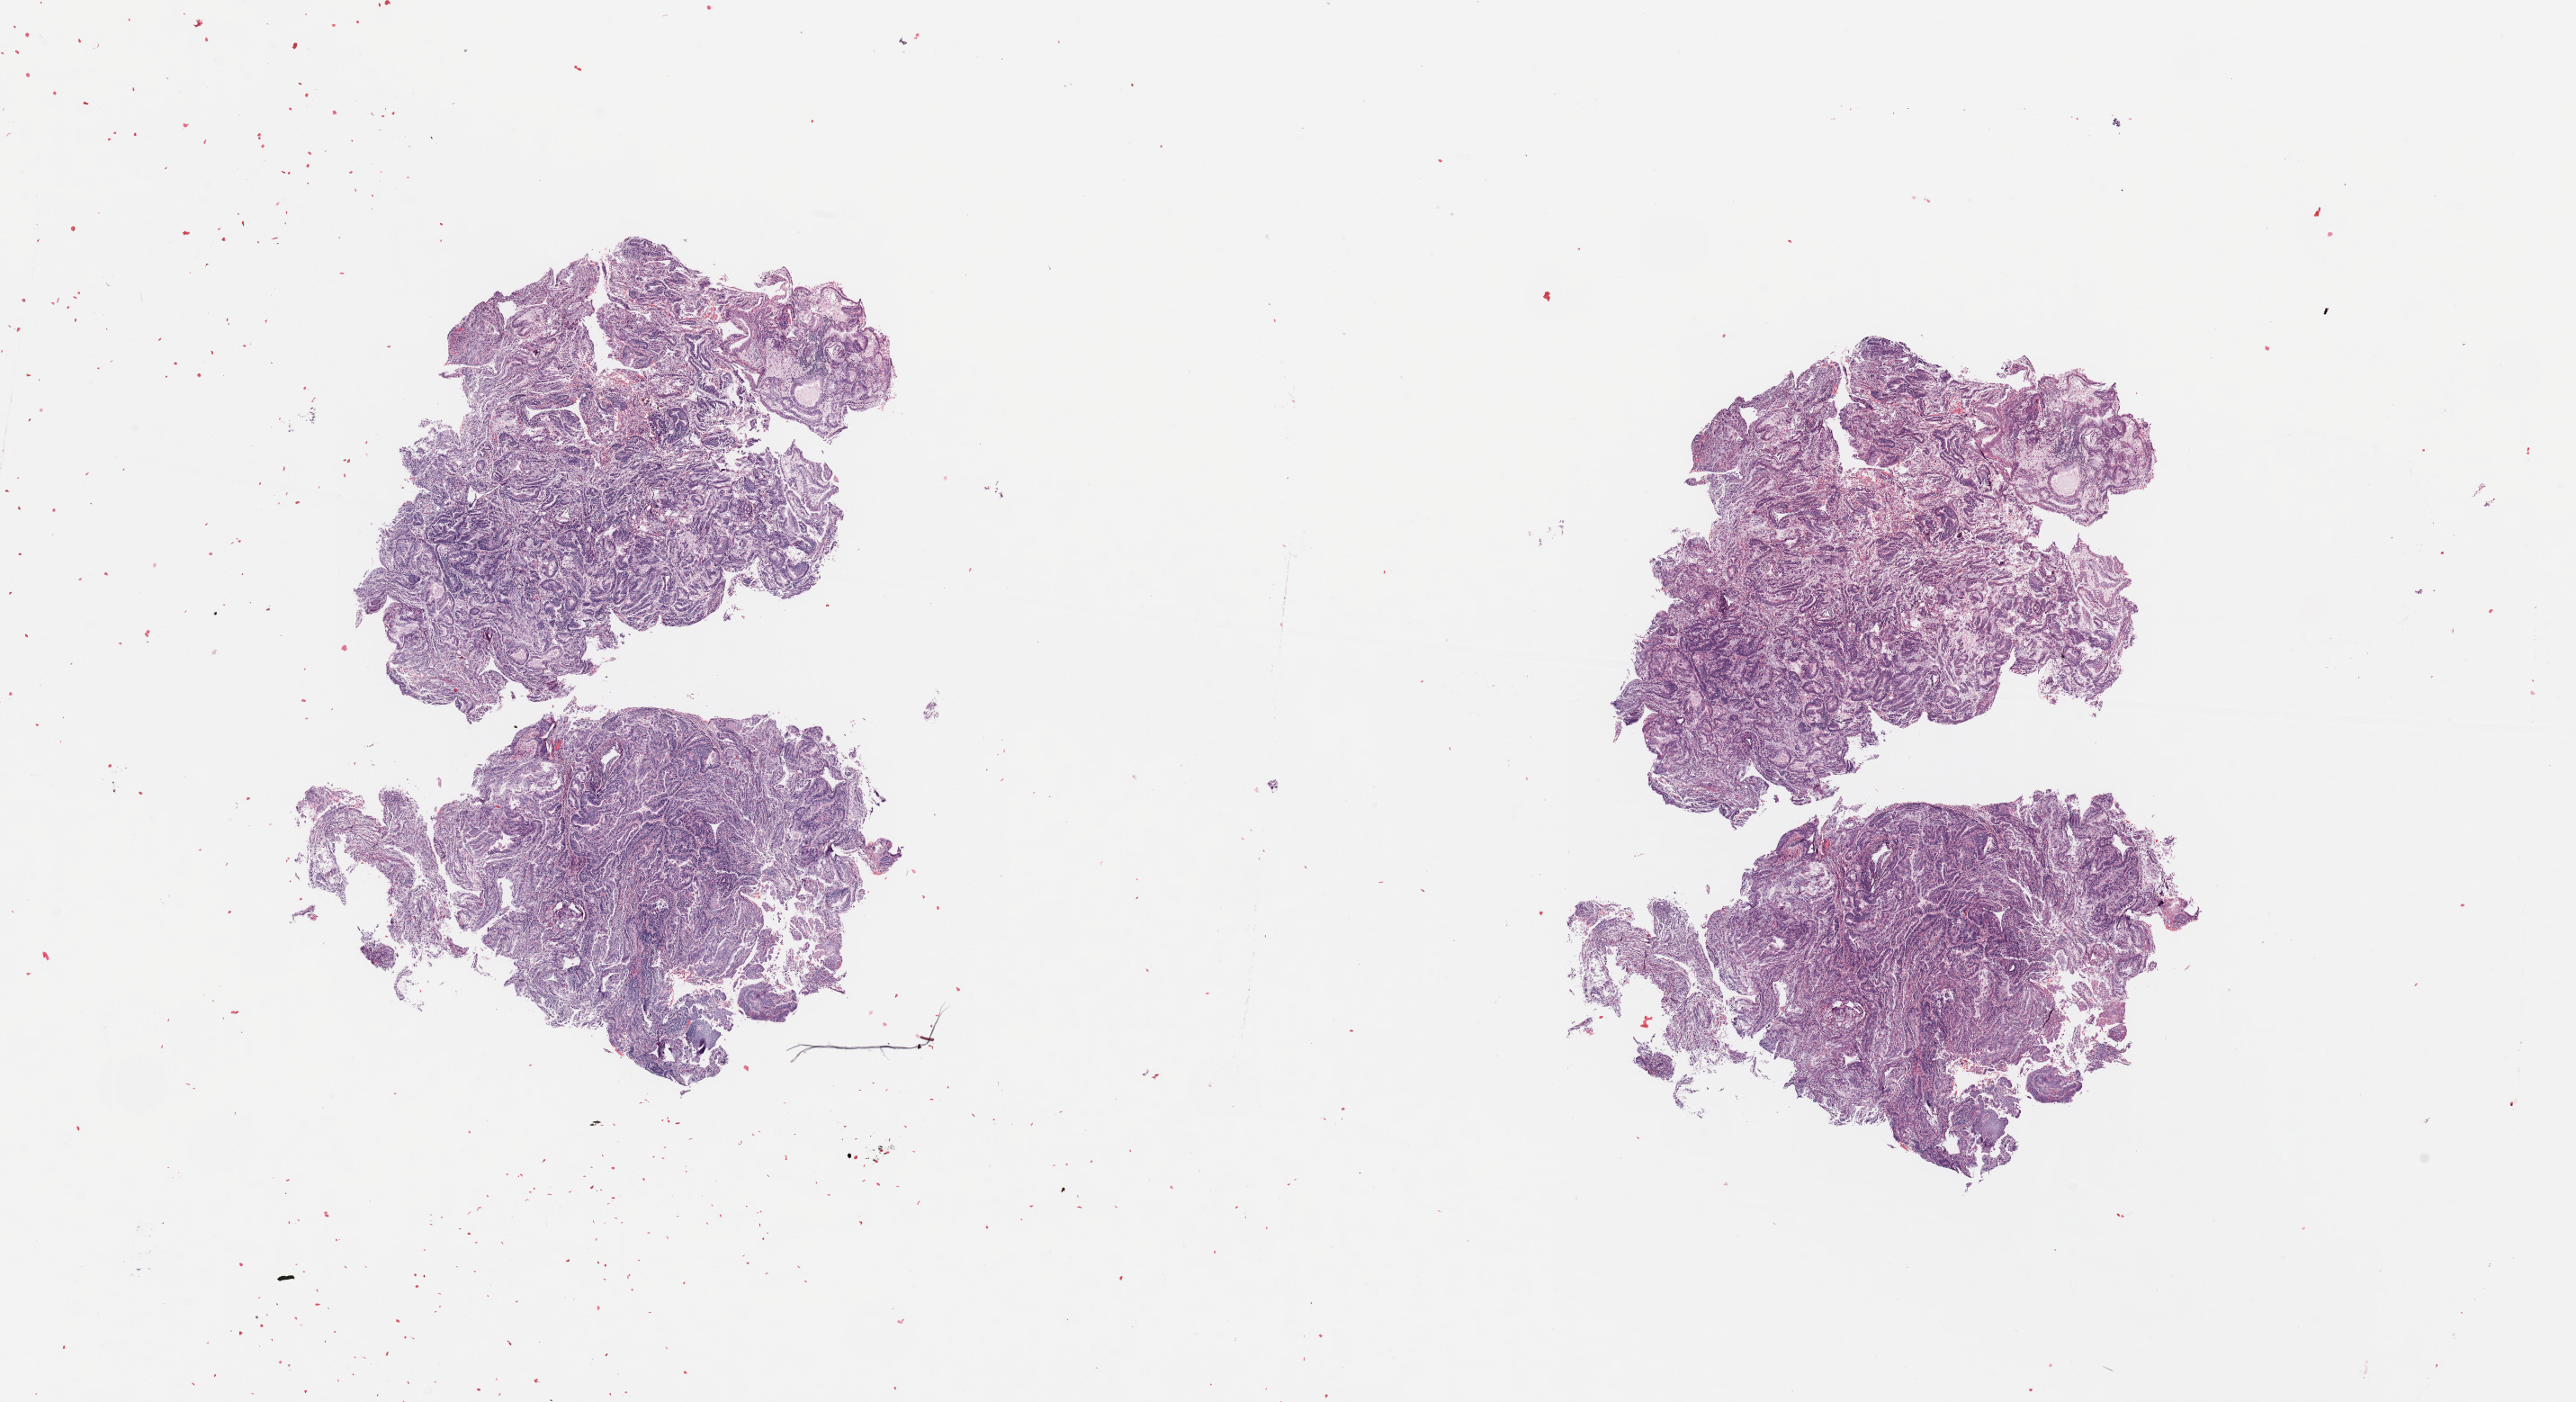
Digitized Hematoxylin and eosin (H&E) stained tissue section (whole slide) — shown as a low-resolution overview of the whole scanned area (about 22.6 x 12.3 mm, slide scanned at 20x). Uterus, tumour tissue. 77-year-old female patient. Histologic grade: G1 (well differentiated).
AJCC pathologic stage: I. Diagnosis: Endometrioid adenocarcinoma, NOS.